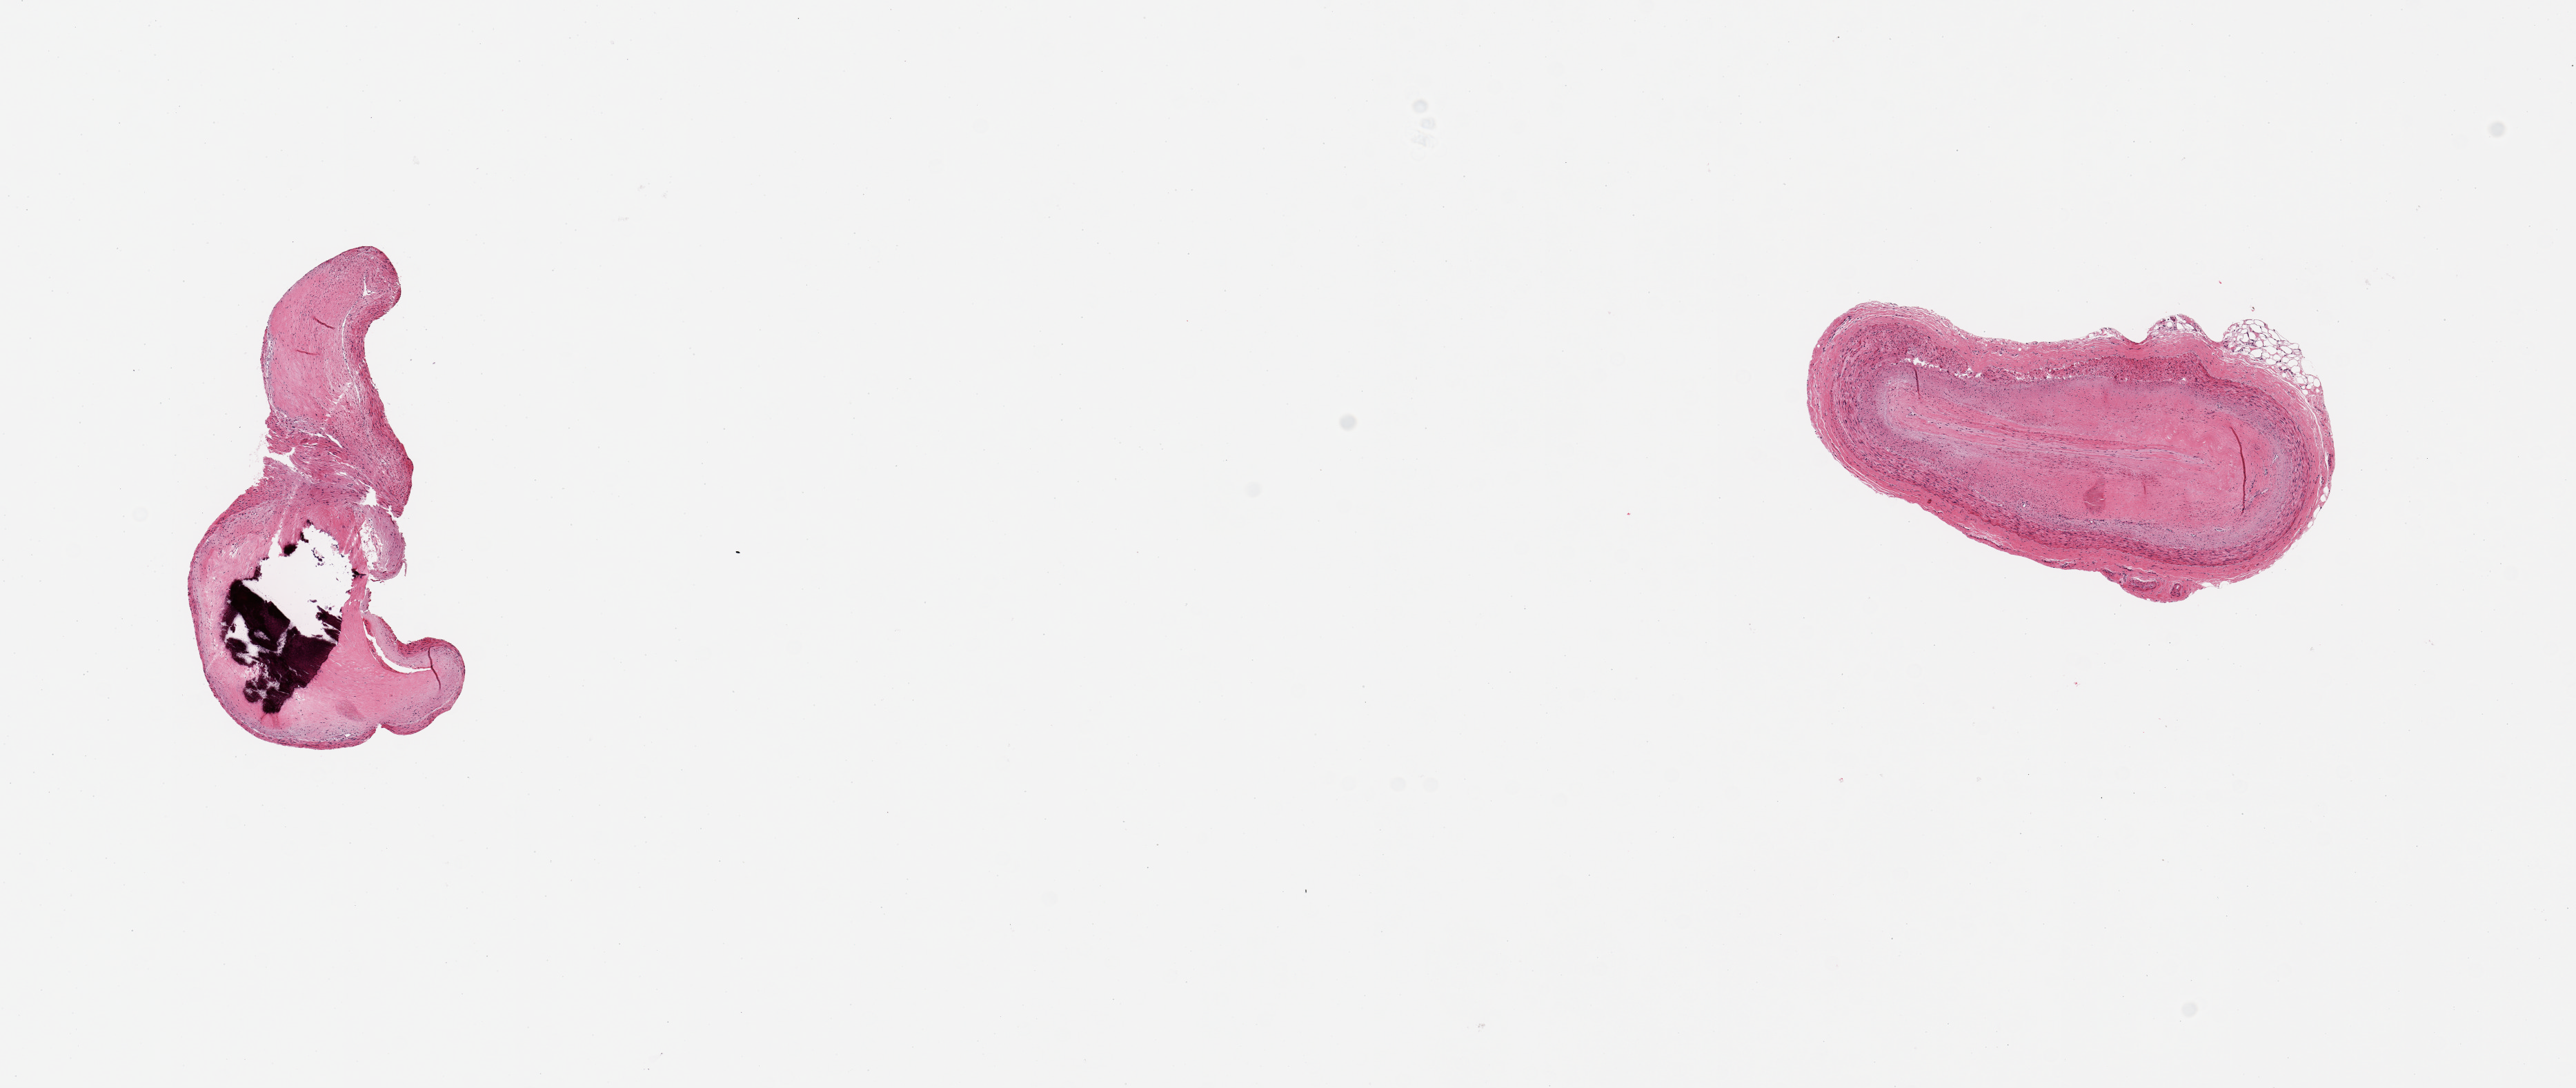
Hematoxylin and eosin (H&E) whole-slide image — low-resolution overview of the scanned area, about 14.8 x 6.2 mm (acquisition: 20x scan). PAXgene-fixed, paraffin-embedded tissue. Section of coronary artery (target tissue). Tissue donor sample. Male donor.
Pathologist's review note for this sample: 2 piecesm subtotally occlusive calcified atherosis.